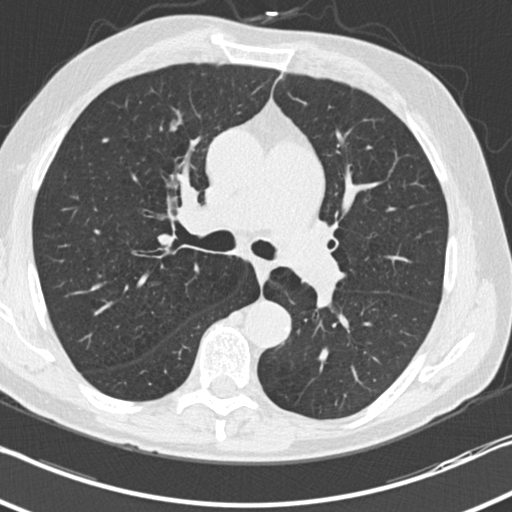
Low-dose screening chest CT, axial slice, third annual screen, lung window (W 1500 / L -600 HU), standard (soft-tissue) reconstruction kernel (B30f), 120 kVp, slice 85 of 212 in the series. Male participant, aged 70 years at enrolment. Current smoker at enrolment.
• Lesion marked by an expert reader, box from (x=157, y=104) to (x=203, y=143) px.
• Screening reader's record for this exam (one nodule recorded; not confirmed to be the boxed lesion): non-calcified nodule or mass ≥4 mm, right middle lobe, 9 × 8 mm, smooth margins, soft tissue attenuation, pre-existing on the prior screen: no.
• Participant outcome: lung cancer diagnosed 53 days after this screen — squamous cell carcinoma, NOS, right upper lobe, moderately differentiated (G2), stage IA (AJCC 6th edition), 10 mm at pathology.